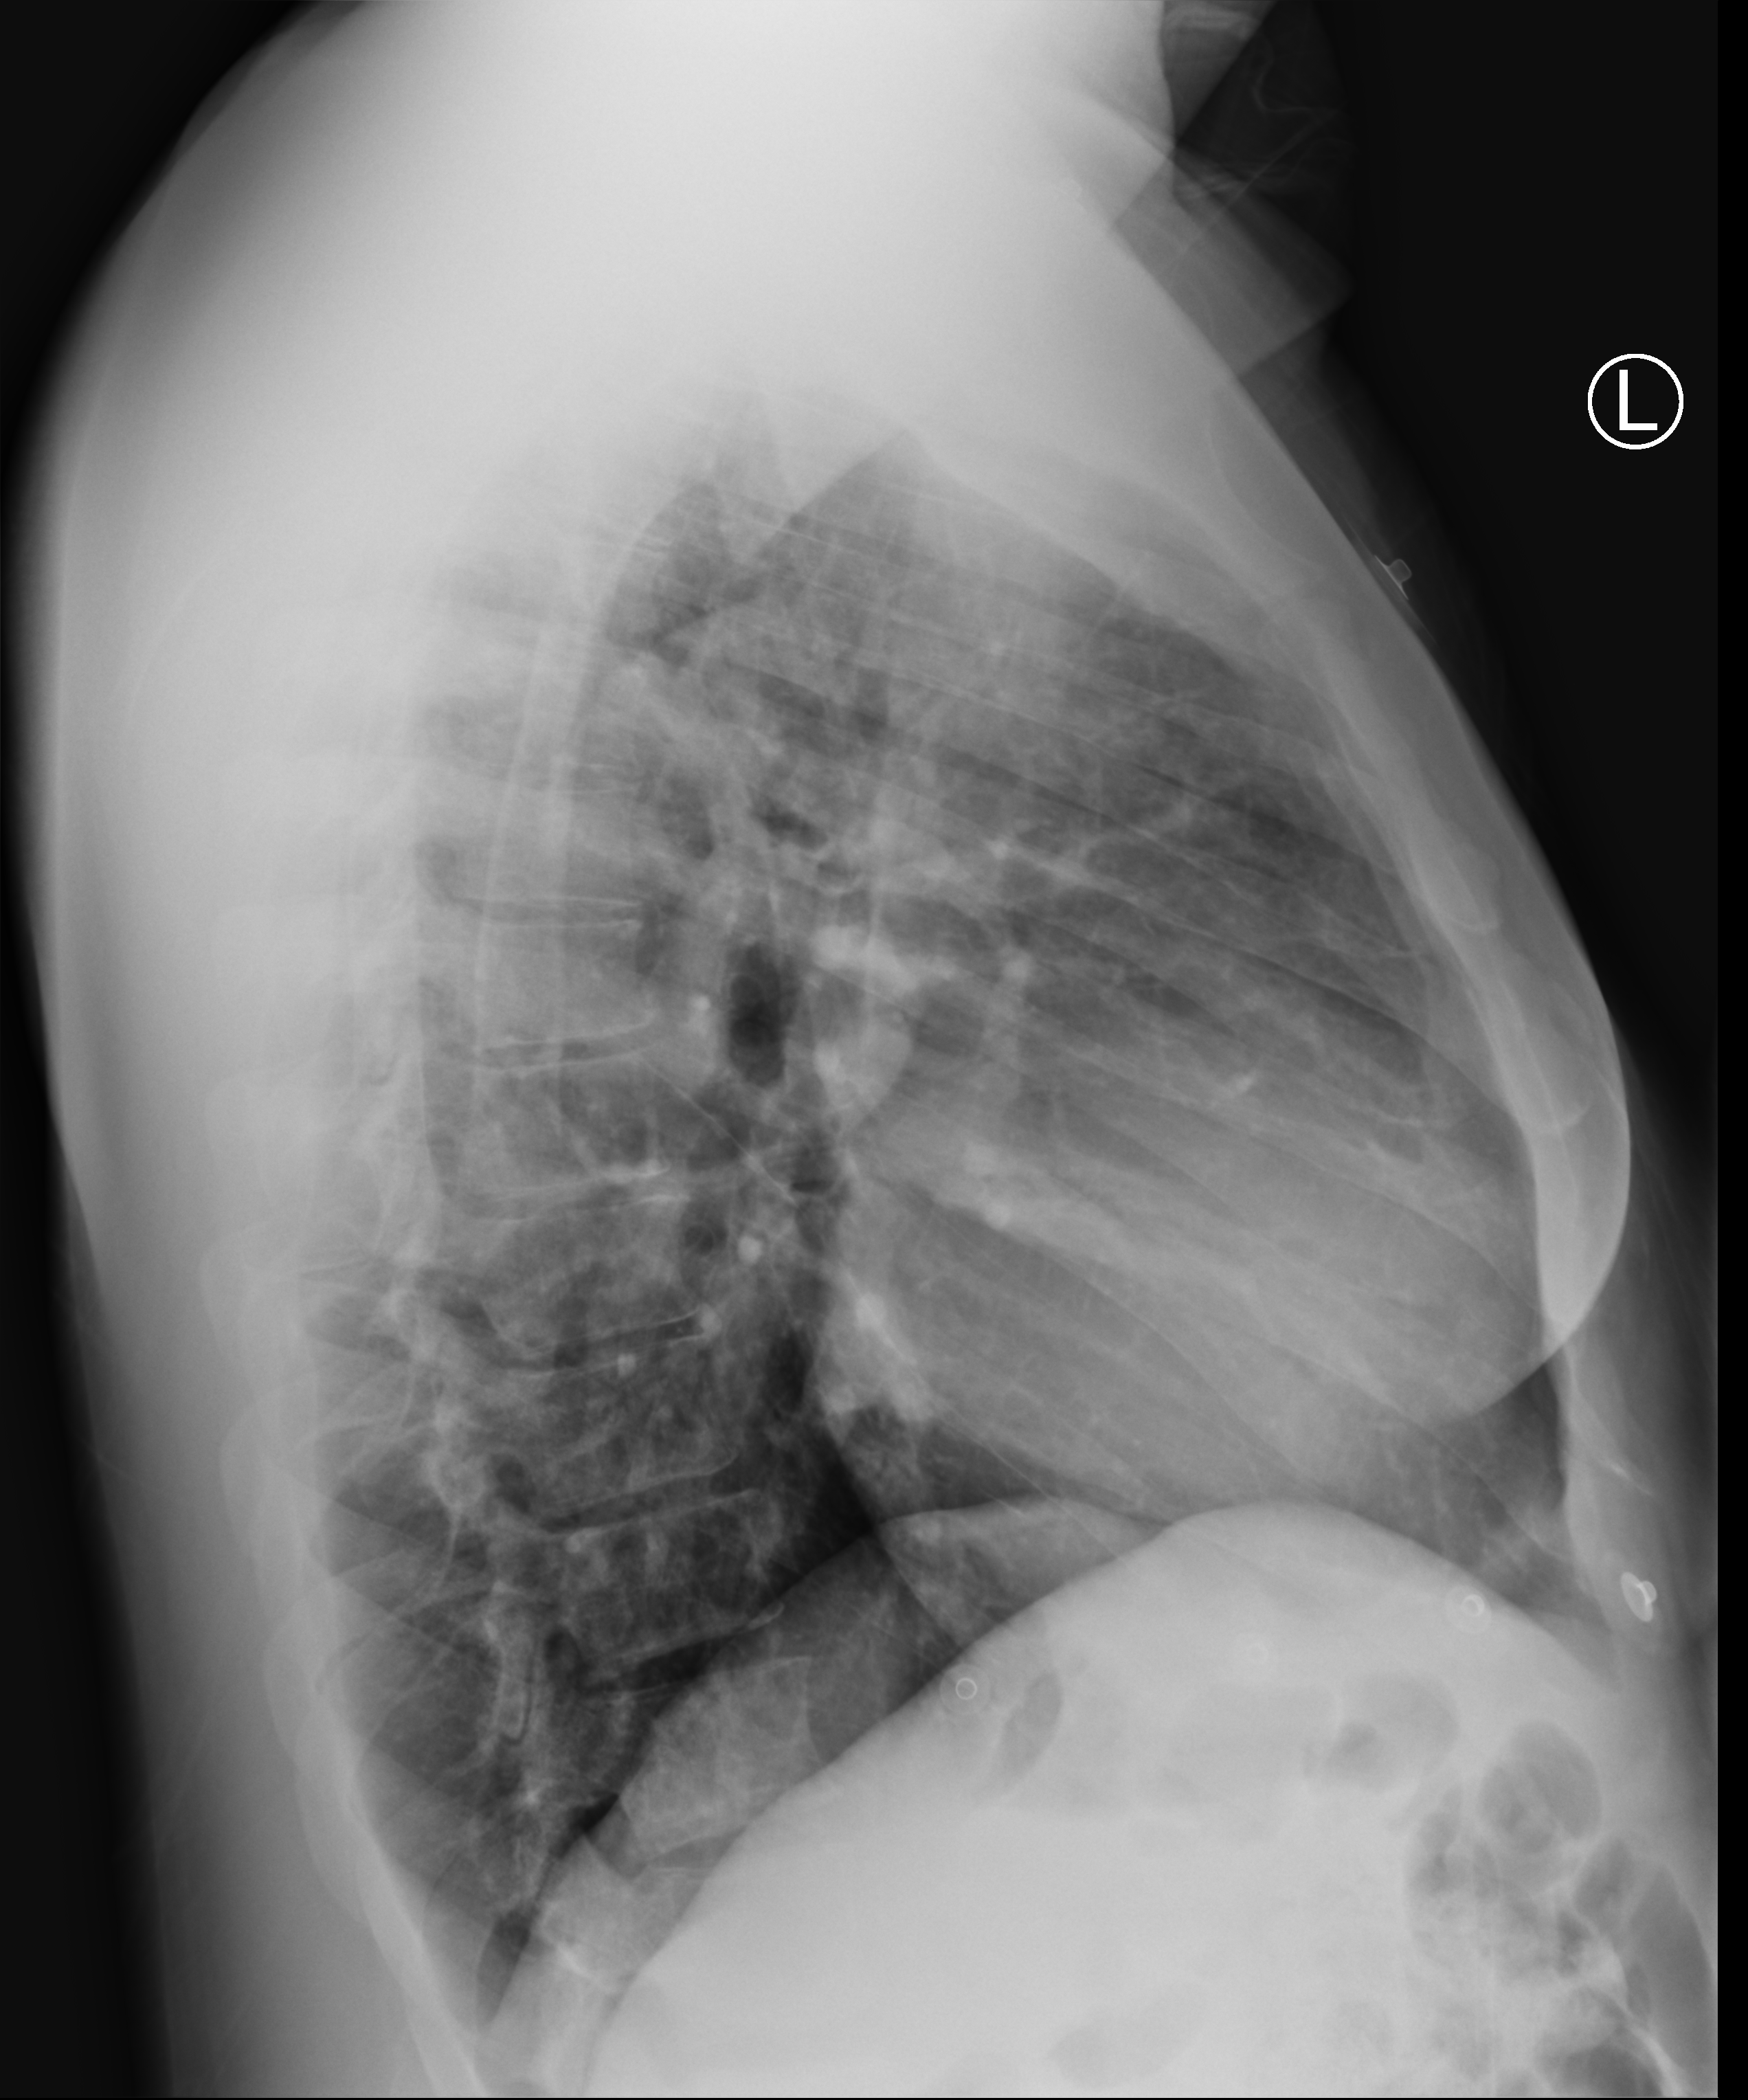
Chest X-ray. Male patient hospitalised with COVID-19, age 18–59 years.
Admission-level facts for this patient (not findings on this image; timing relative to this image not recorded): admitted to intensive care during this hospital stay: no.